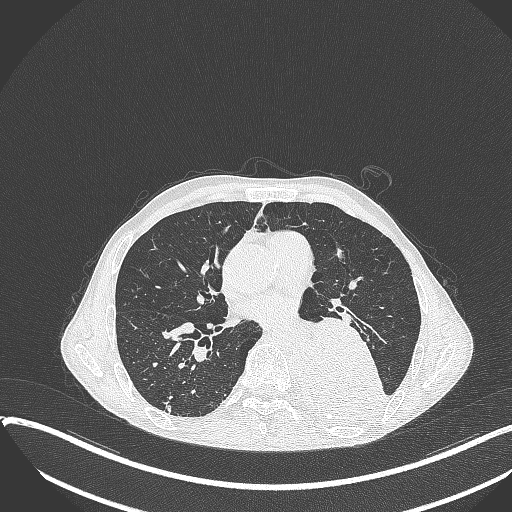
Chest CT, one axial slice. Slice 185 of 401 in the series (ordered by position). 120 kVp. Lung window (W 1500 / L -600 HU). 512 × 512 image matrix, field of view 400 × 400 mm. Patient: male, 57 years. Case-level facts recorded for this patient, not image findings: clinical TNM (as recorded): T4 N0 M0.
Outlined on this slice (bounding box drawn by a radiologist):
- lung tumour (recorded histology: squamous cell carcinoma): box from (x=294, y=316) to (x=396, y=429) px